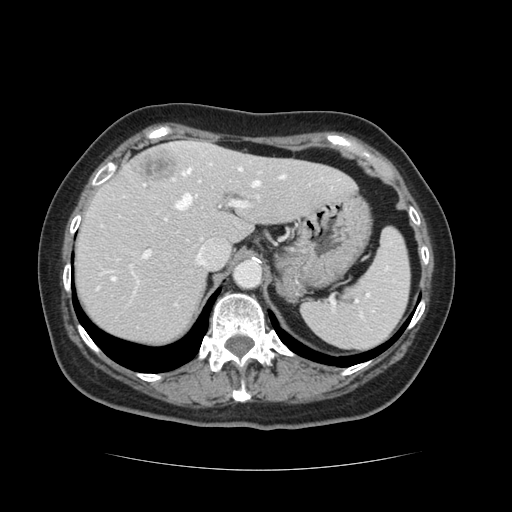
Contrast-enhanced abdominal CT, one axial slice; position 92 of 128 along the scan axis; 120 kVp; soft-tissue window (W 400 / L 40 HU); 2.5 mm slice thickness; 512 × 512 image matrix, field of view 366 × 366 mm. Female patient, age 67 years. From the clinical record (not read from this slice): diagnosis: colorectal cancer liver metastases, imaged before liver resection; multiple liver metastases: yes.
Structures marked on this image (expert manual segmentation):
- hepatic veins: box from (x=112, y=168) to (x=286, y=284) px
- liver: (x=75, y=143)–(x=352, y=346)
- planned liver remnant (the part of the liver to remain after resection): (x=75, y=157)–(x=352, y=346)
- portal vein (with intrahepatic branches): (x=145, y=162)–(x=261, y=257)
- liver metastasis: (x=134, y=155)–(x=181, y=183)